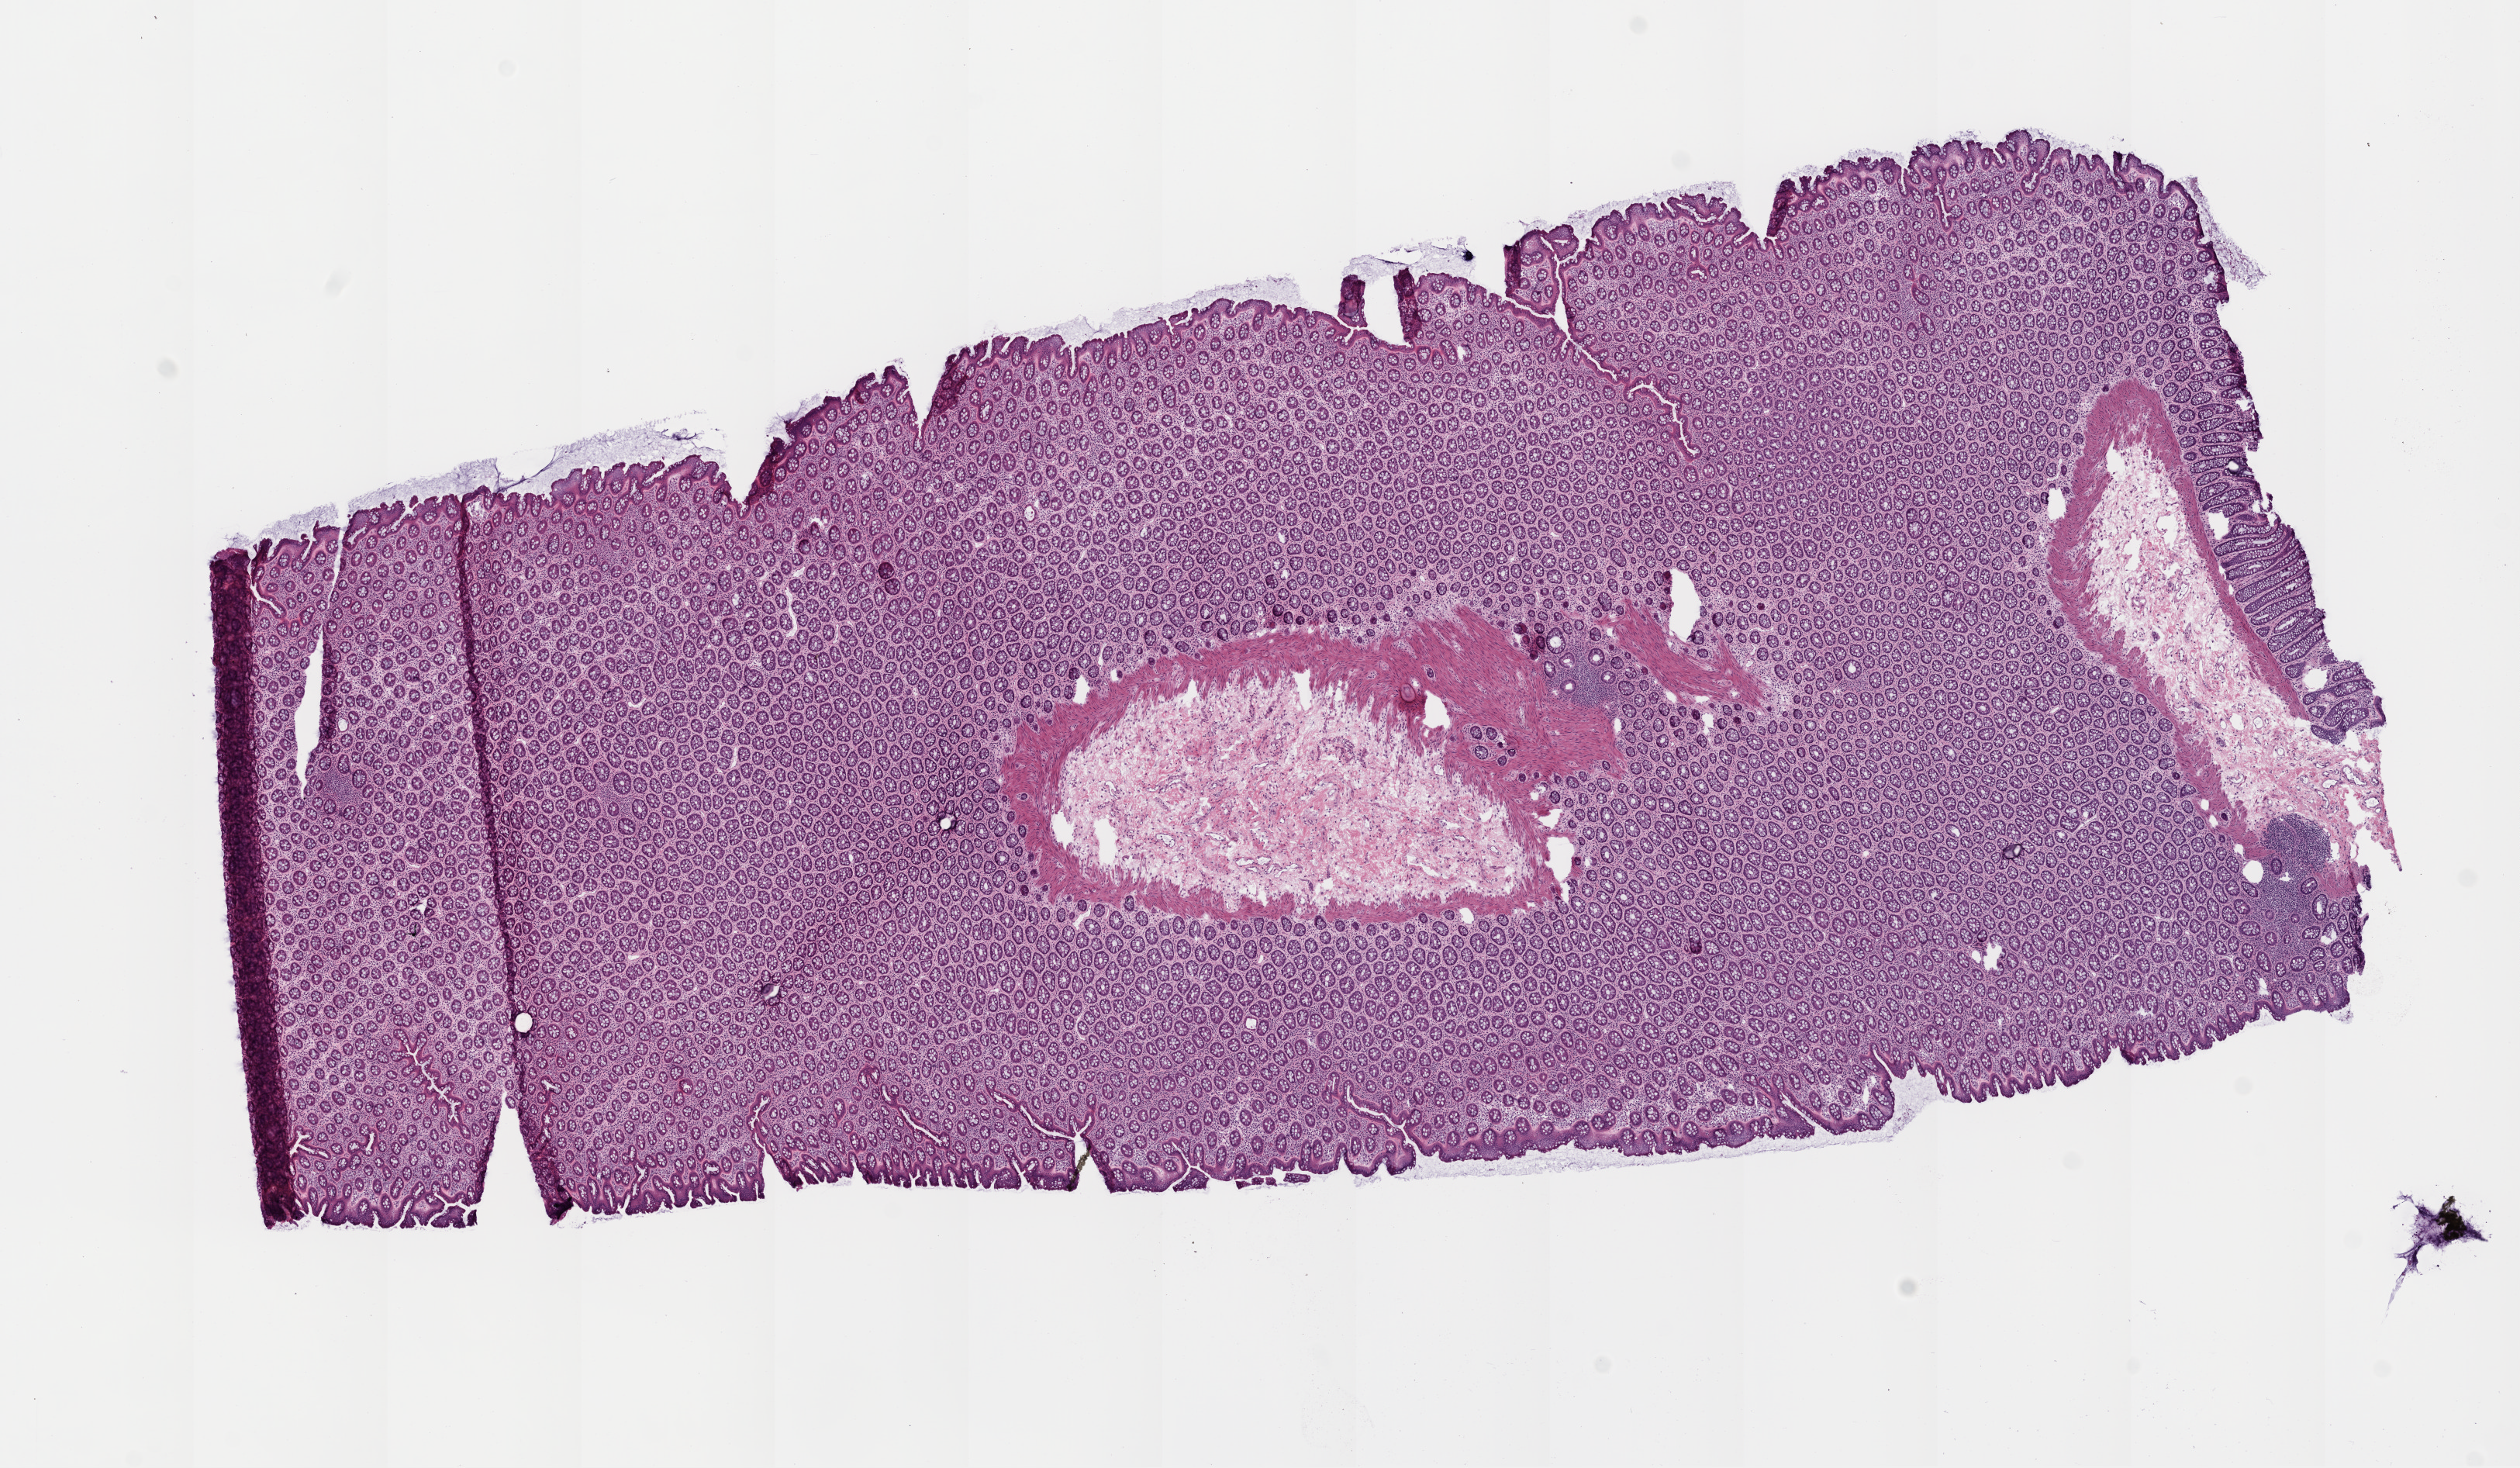
Whole-slide histology image, H&E-stained — low-resolution overview of the scanned area, about 13.0 x 7.6 mm (from a 20x scan); frozen section from the top of the tissue portion; sample: solid tissue normal (non-tumour tissue), rectum. Male patient; age at initial diagnosis 54 years.
- this section: solid tissue normal sample (biorepository sample class)
- patient diagnosis: Mucinous adenocarcinoma (rectosigmoid junction)